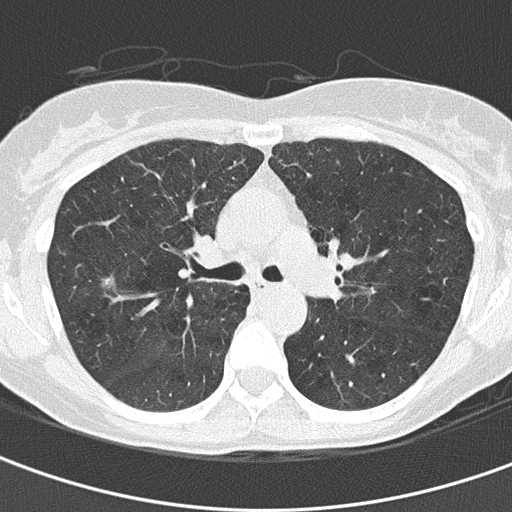
Low-dose screening chest CT, axial slice; baseline screening round; lung window (W 1500 / L -600 HU). Female, age 59 years at enrolment. Current smoker at enrolment.
• Lesion marked by an expert reader, bounding box [x1, y1, x2, y2] px = [87, 264, 129, 302].
• No non-calcified nodule or mass ≥4 mm was recorded by the screening reader at this exam.
• Participant outcome: lung cancer diagnosed 834 days after this screen — bronchiolo-alveolar adenocarcinoma, NOS, right upper lobe, well differentiated (G1), stage IA (AJCC 6th edition), 4 mm at pathology.